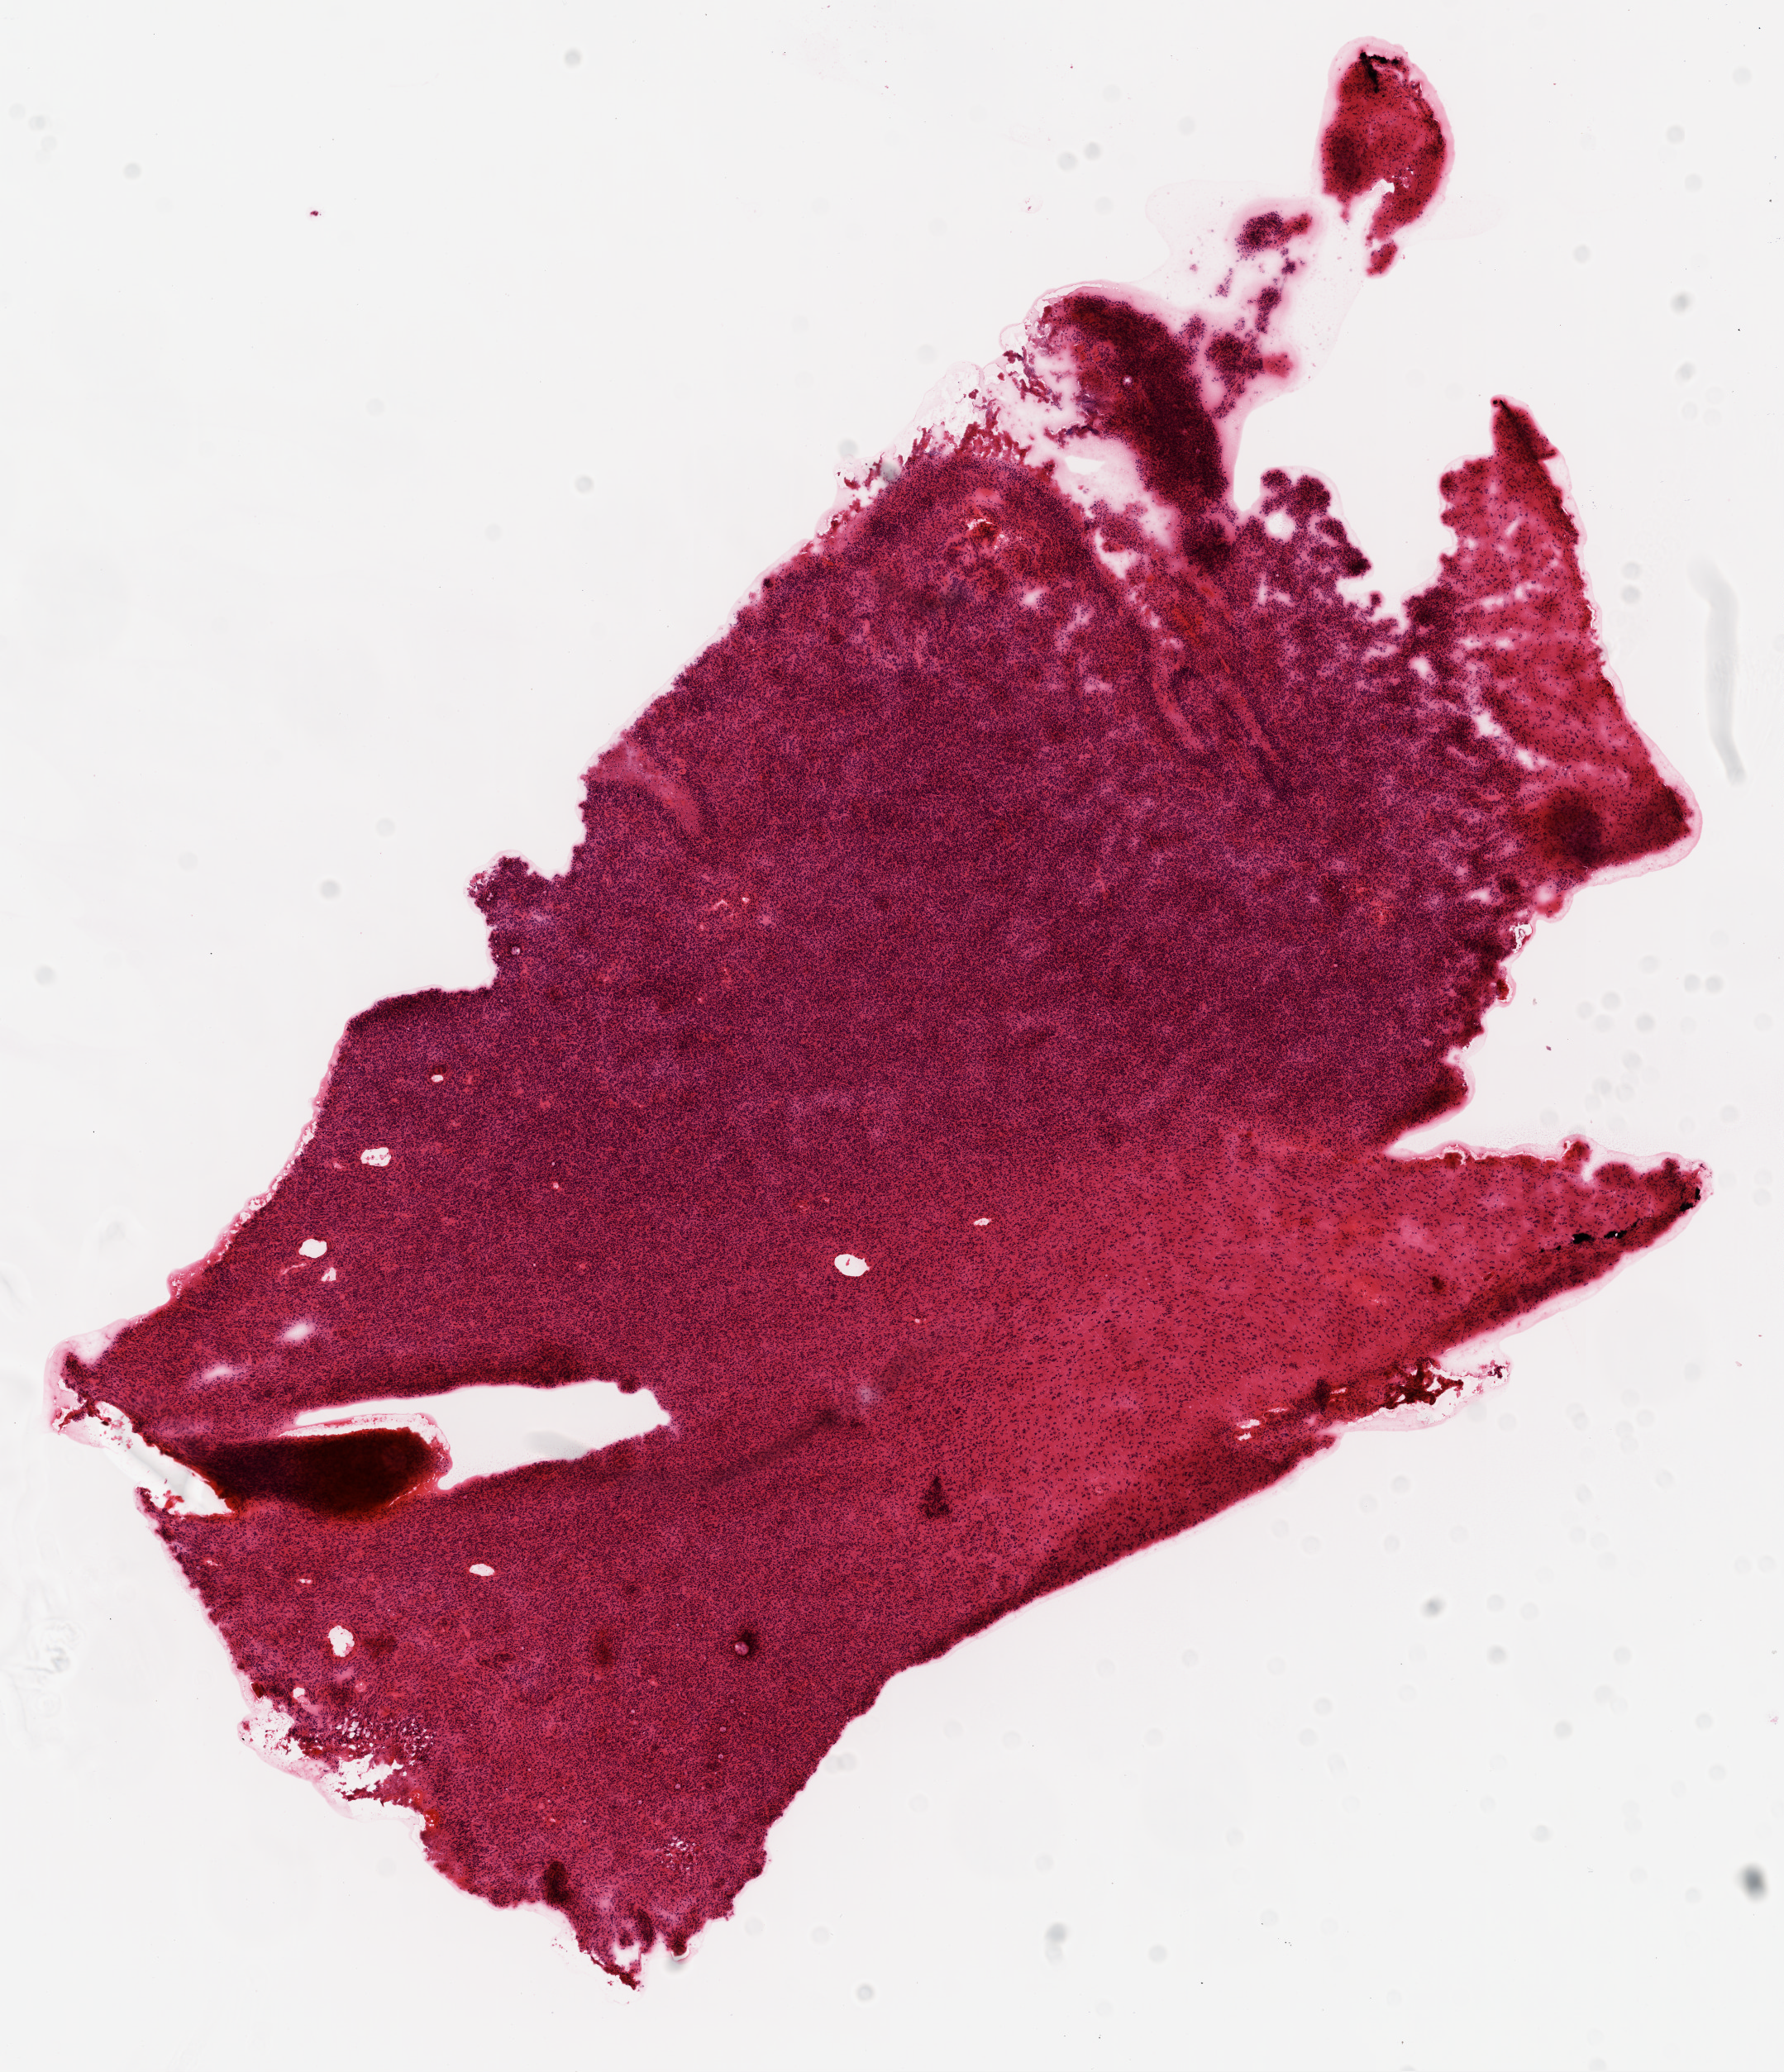
Hematoxylin and eosin (H&E) stained whole-slide image, whole scanned area (about 8.7 x 10.1 mm, acquisition: 20x scan) shown as a low-resolution overview. Frozen section from the top of the tissue portion. Sample: primary tumour, brain. Male patient; age at initial diagnosis 62 years. Slide review estimates, as recorded: tumour cells 88%, tumour nuclei 90%, normal cells 0%, stromal cells 10%, necrosis 2%.
Histologic diagnosis: Glioblastoma.